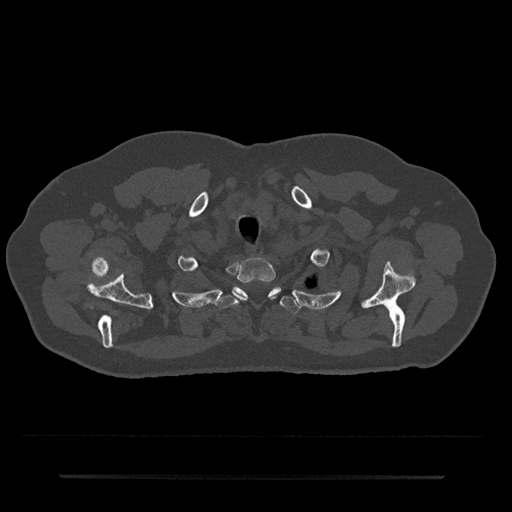
CT including the spine, one axial slice. Position 623 of 797 along the scan axis. Bone window (W 1800 / L 400 HU). 0.5 mm slice thickness. 512 × 512 image matrix, field of view 437 × 437 mm. Male patient, age 69 years. From the clinical record (not read from this slice): primary cancer: prostate.
Annotated regions visible in this slice (semi-automatic segmentation, software-assisted and operator-edited):
- T1 vertebra: bounding box [x1, y1, x2, y2] px = [237, 258, 280, 299]
- T2 vertebra: [216, 287, 300, 313]